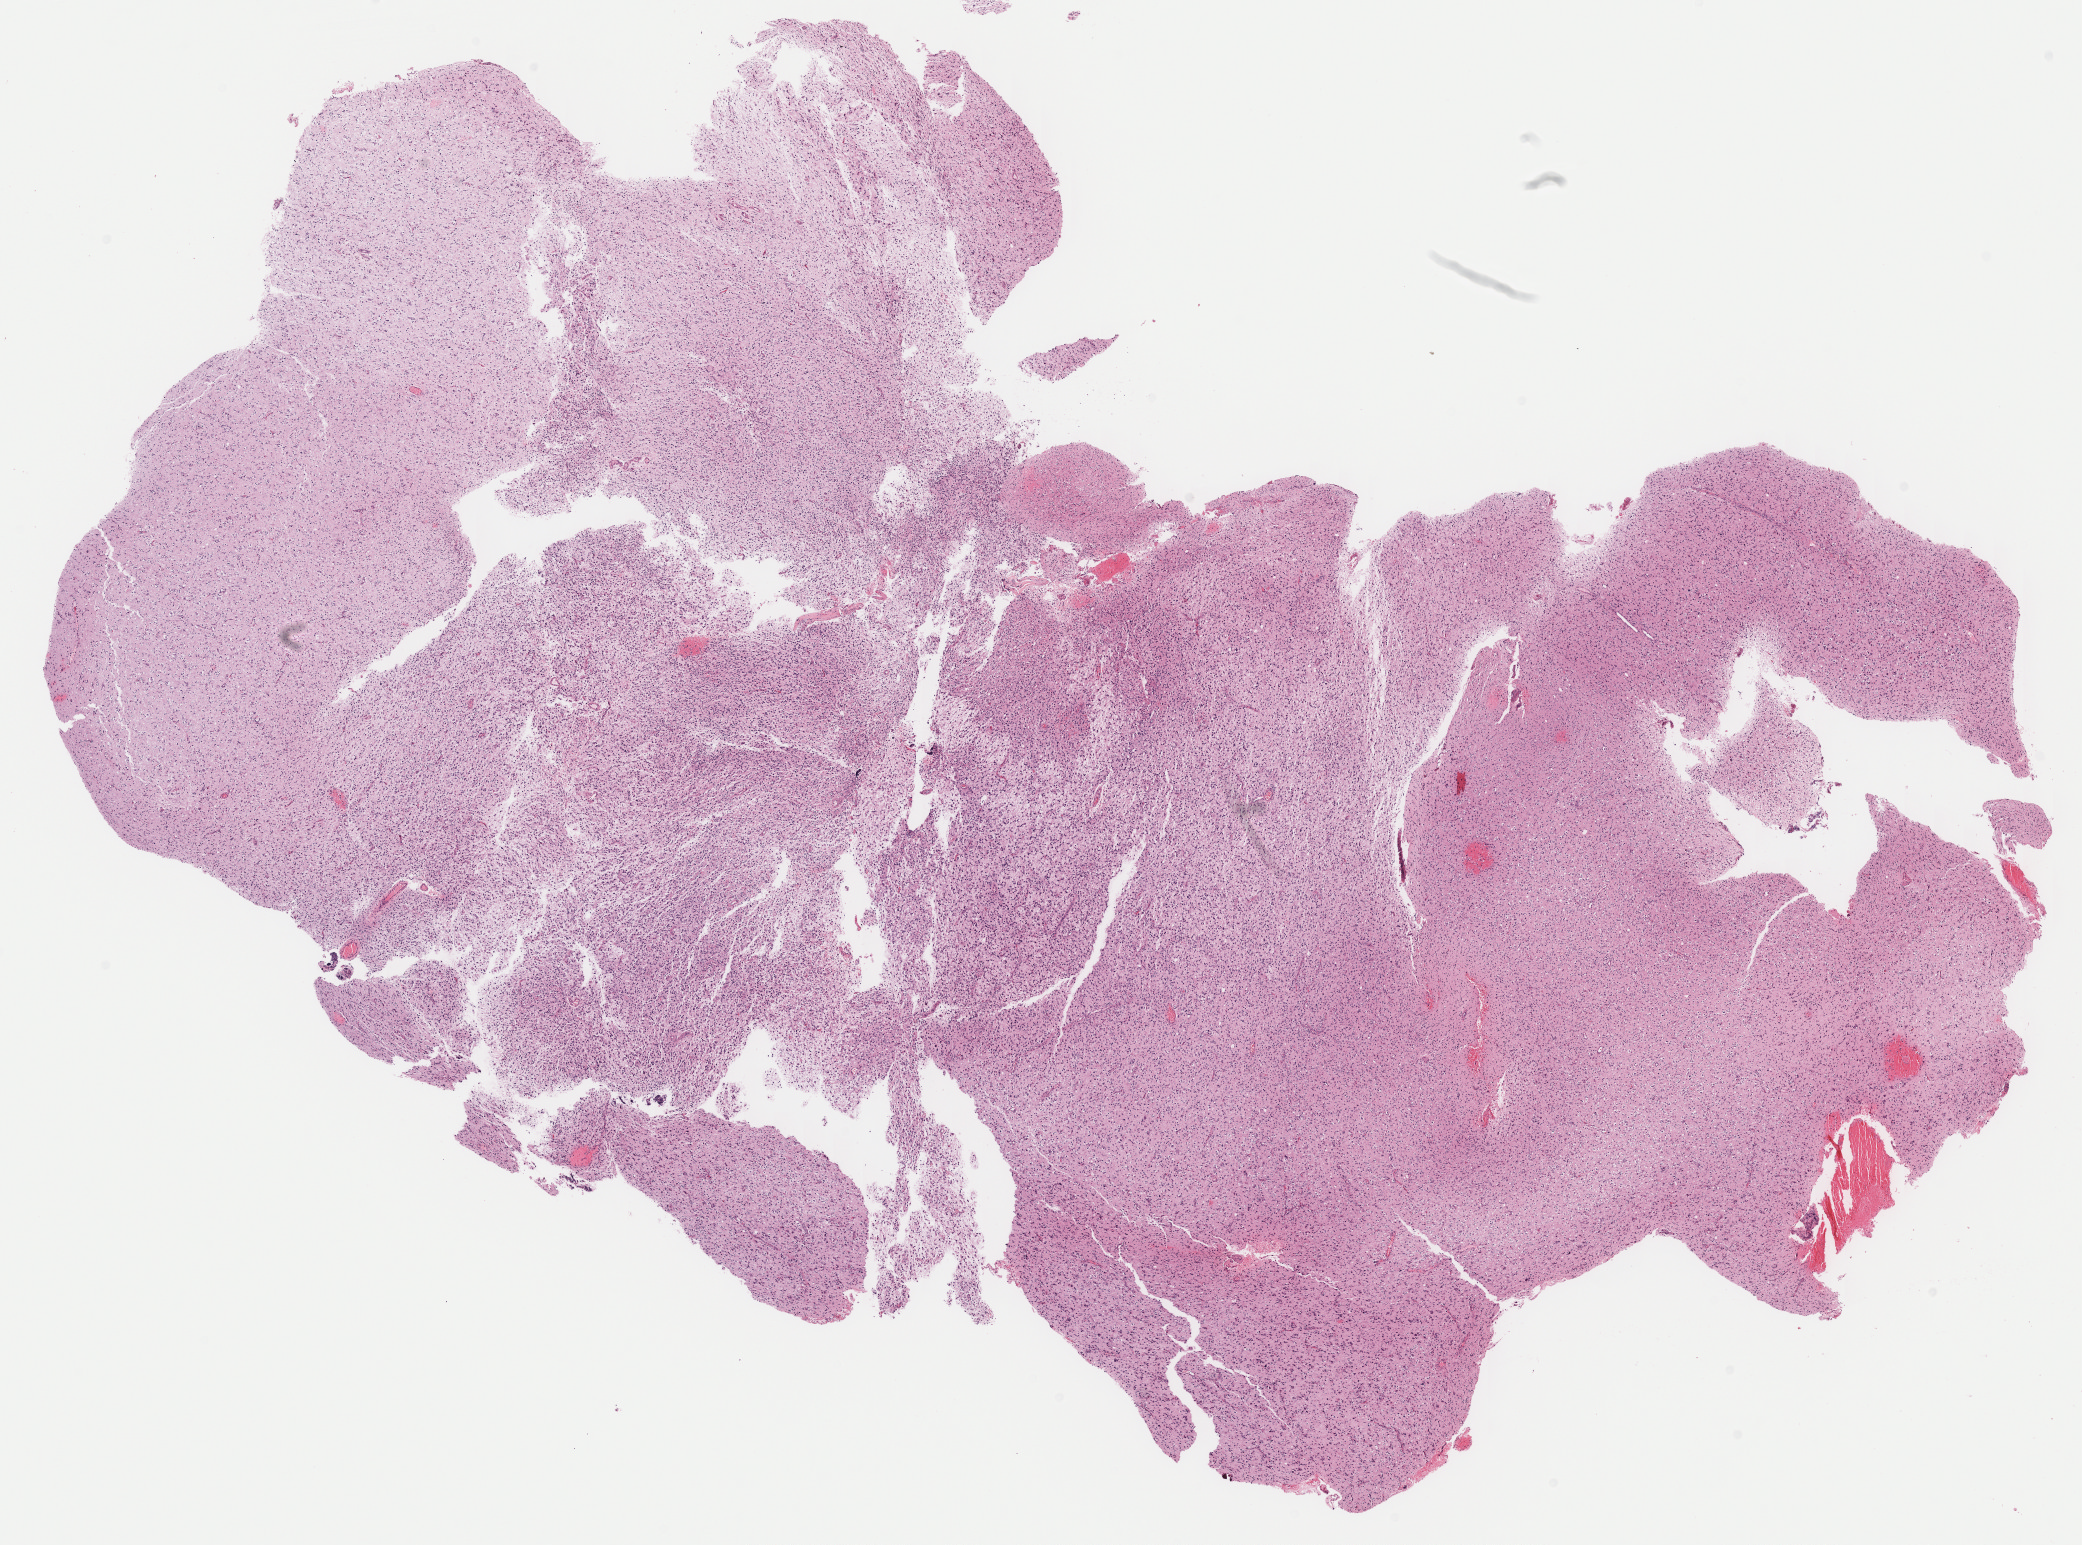
Whole-slide histology image, H&E-stained, whole scanned area (about 16.4 x 12.2 mm, slide scanned at 40x) shown as a low-resolution overview; formalin-fixed paraffin-embedded (FFPE) diagnostic section; brain, primary tumour sample. Female, age 27 years at initial diagnosis. Histologic grade: G3 (poorly differentiated).
* histologic diagnosis: Mixed glioma (temporal lobe)
* laterality: left